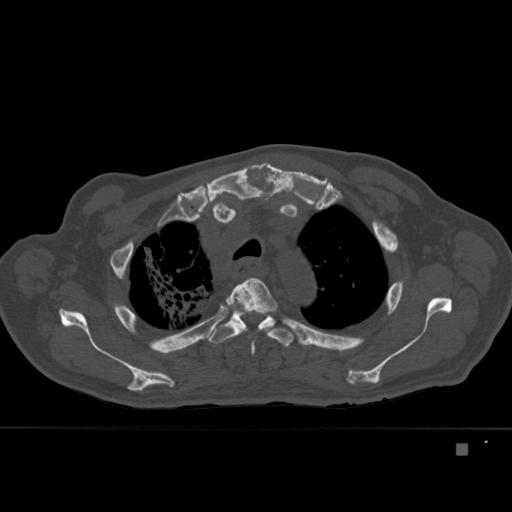
CT including the spine, one axial slice. Slice 328 of 451 in the series (ordered by position). Bone window (W 1800 / L 400 HU). 1.5 mm slice thickness. 512 × 512 image matrix, field of view 378 × 378 mm. Patient: male, 75 years. Case-level facts recorded for this patient, not image findings: primary cancer: prostate.
Structures marked on this image (semi-automatic segmentation, software-assisted and operator-edited):
- T3 vertebra: bounding box (x1, y1, x2, y2) in pixels: (222, 278, 277, 356)
- T4 vertebra: (207, 307, 294, 347)